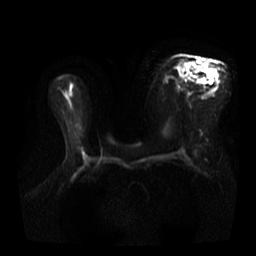
Breast MRI, one axial slice. Diffusion-weighted series; image 2 of 4 stored at this slice position (different b-values; order by instance number). 3 T. 256 × 256 image matrix. Female patient.
Structures marked on this image (outlined manually by an expert reader):
- tumour on diffusion-weighted imaging: bounding box [x1, y1, x2, y2] px = [201, 66, 206, 72]